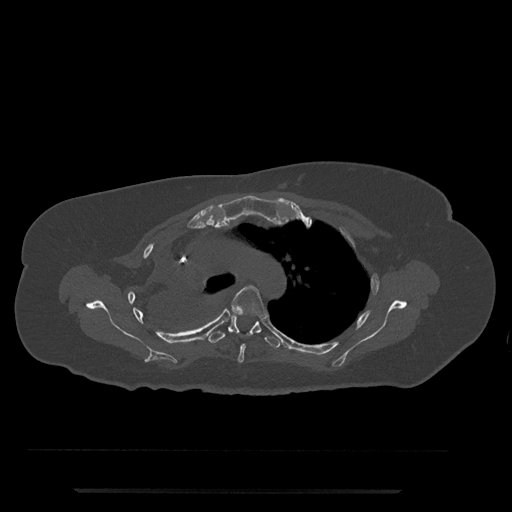
CT including the spine, one axial slice. Slice 566 of 797 in the series (ordered by position). Bone window (W 1800 / L 400 HU). 512 × 512 image matrix. Female patient, age 51 years. Case-level facts recorded for this patient, not image findings: primary cancer: neuro; vertebrae with lytic lesions (as recorded): T8.
Structures marked on this image (semi-automatically segmented with operator editing):
- T4 vertebra: bounding box [x1, y1, x2, y2] px = [229, 285, 268, 363]
- T5 vertebra: [207, 316, 282, 348]